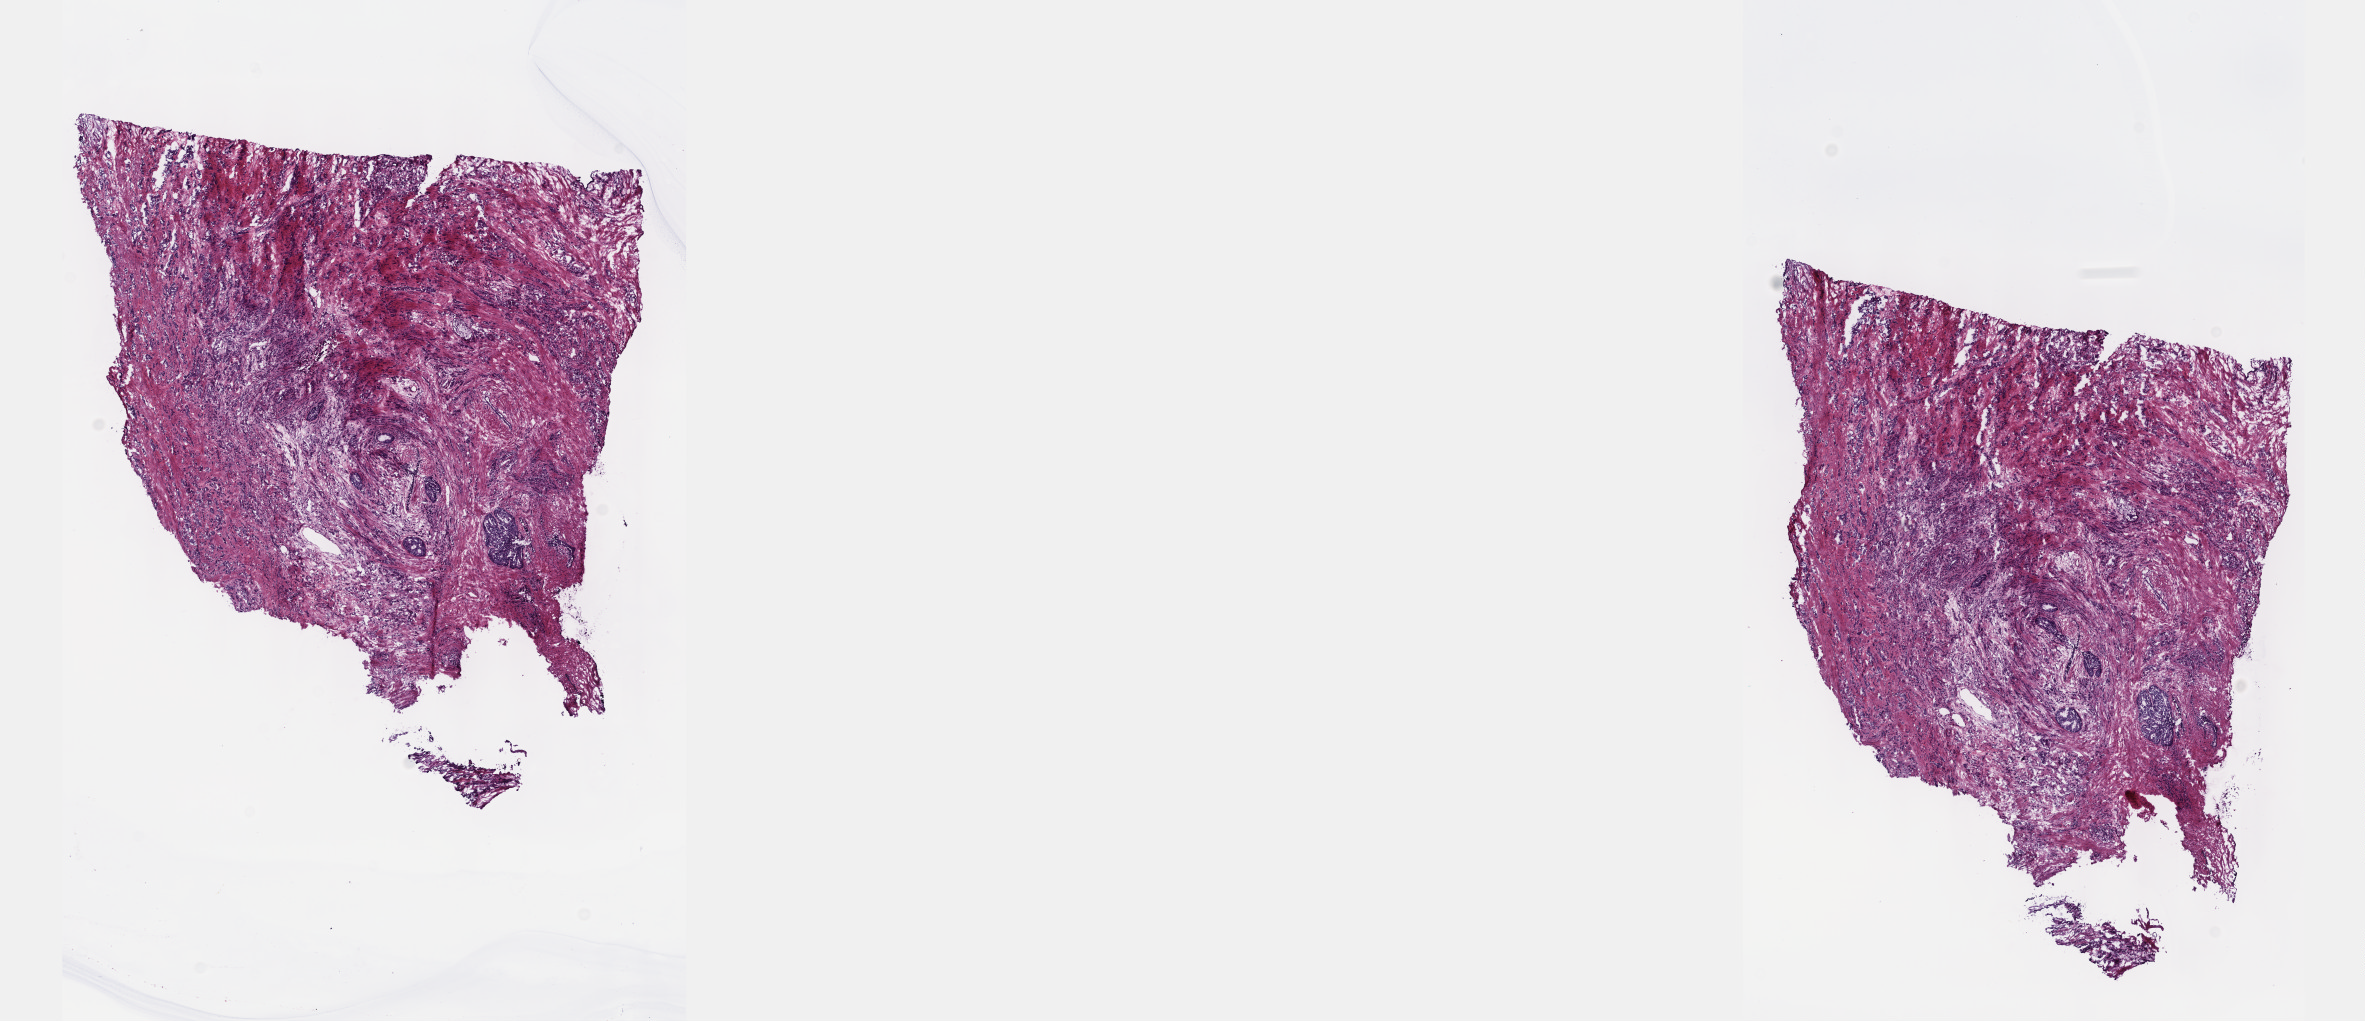
Hematoxylin and eosin (H&E) stained whole-slide image — whole scanned area (about 19.1 x 8.3 mm) shown as a low-resolution overview, frozen section from the top of the tissue portion, prostate, primary tumour sample. Male, age 73 years at initial diagnosis. Gleason score: 7 (3+4). Composition of this section per pathologist review: tumour cells 75%, tumour nuclei 60%, normal cells 25%, stromal cells 0%, necrosis 0%. Infiltration values recorded for this section: lymphocyte infiltration 3%, monocyte infiltration 0%, neutrophil infiltration 0%.
Diagnosis: Adenocarcinoma, NOS (prostate gland).